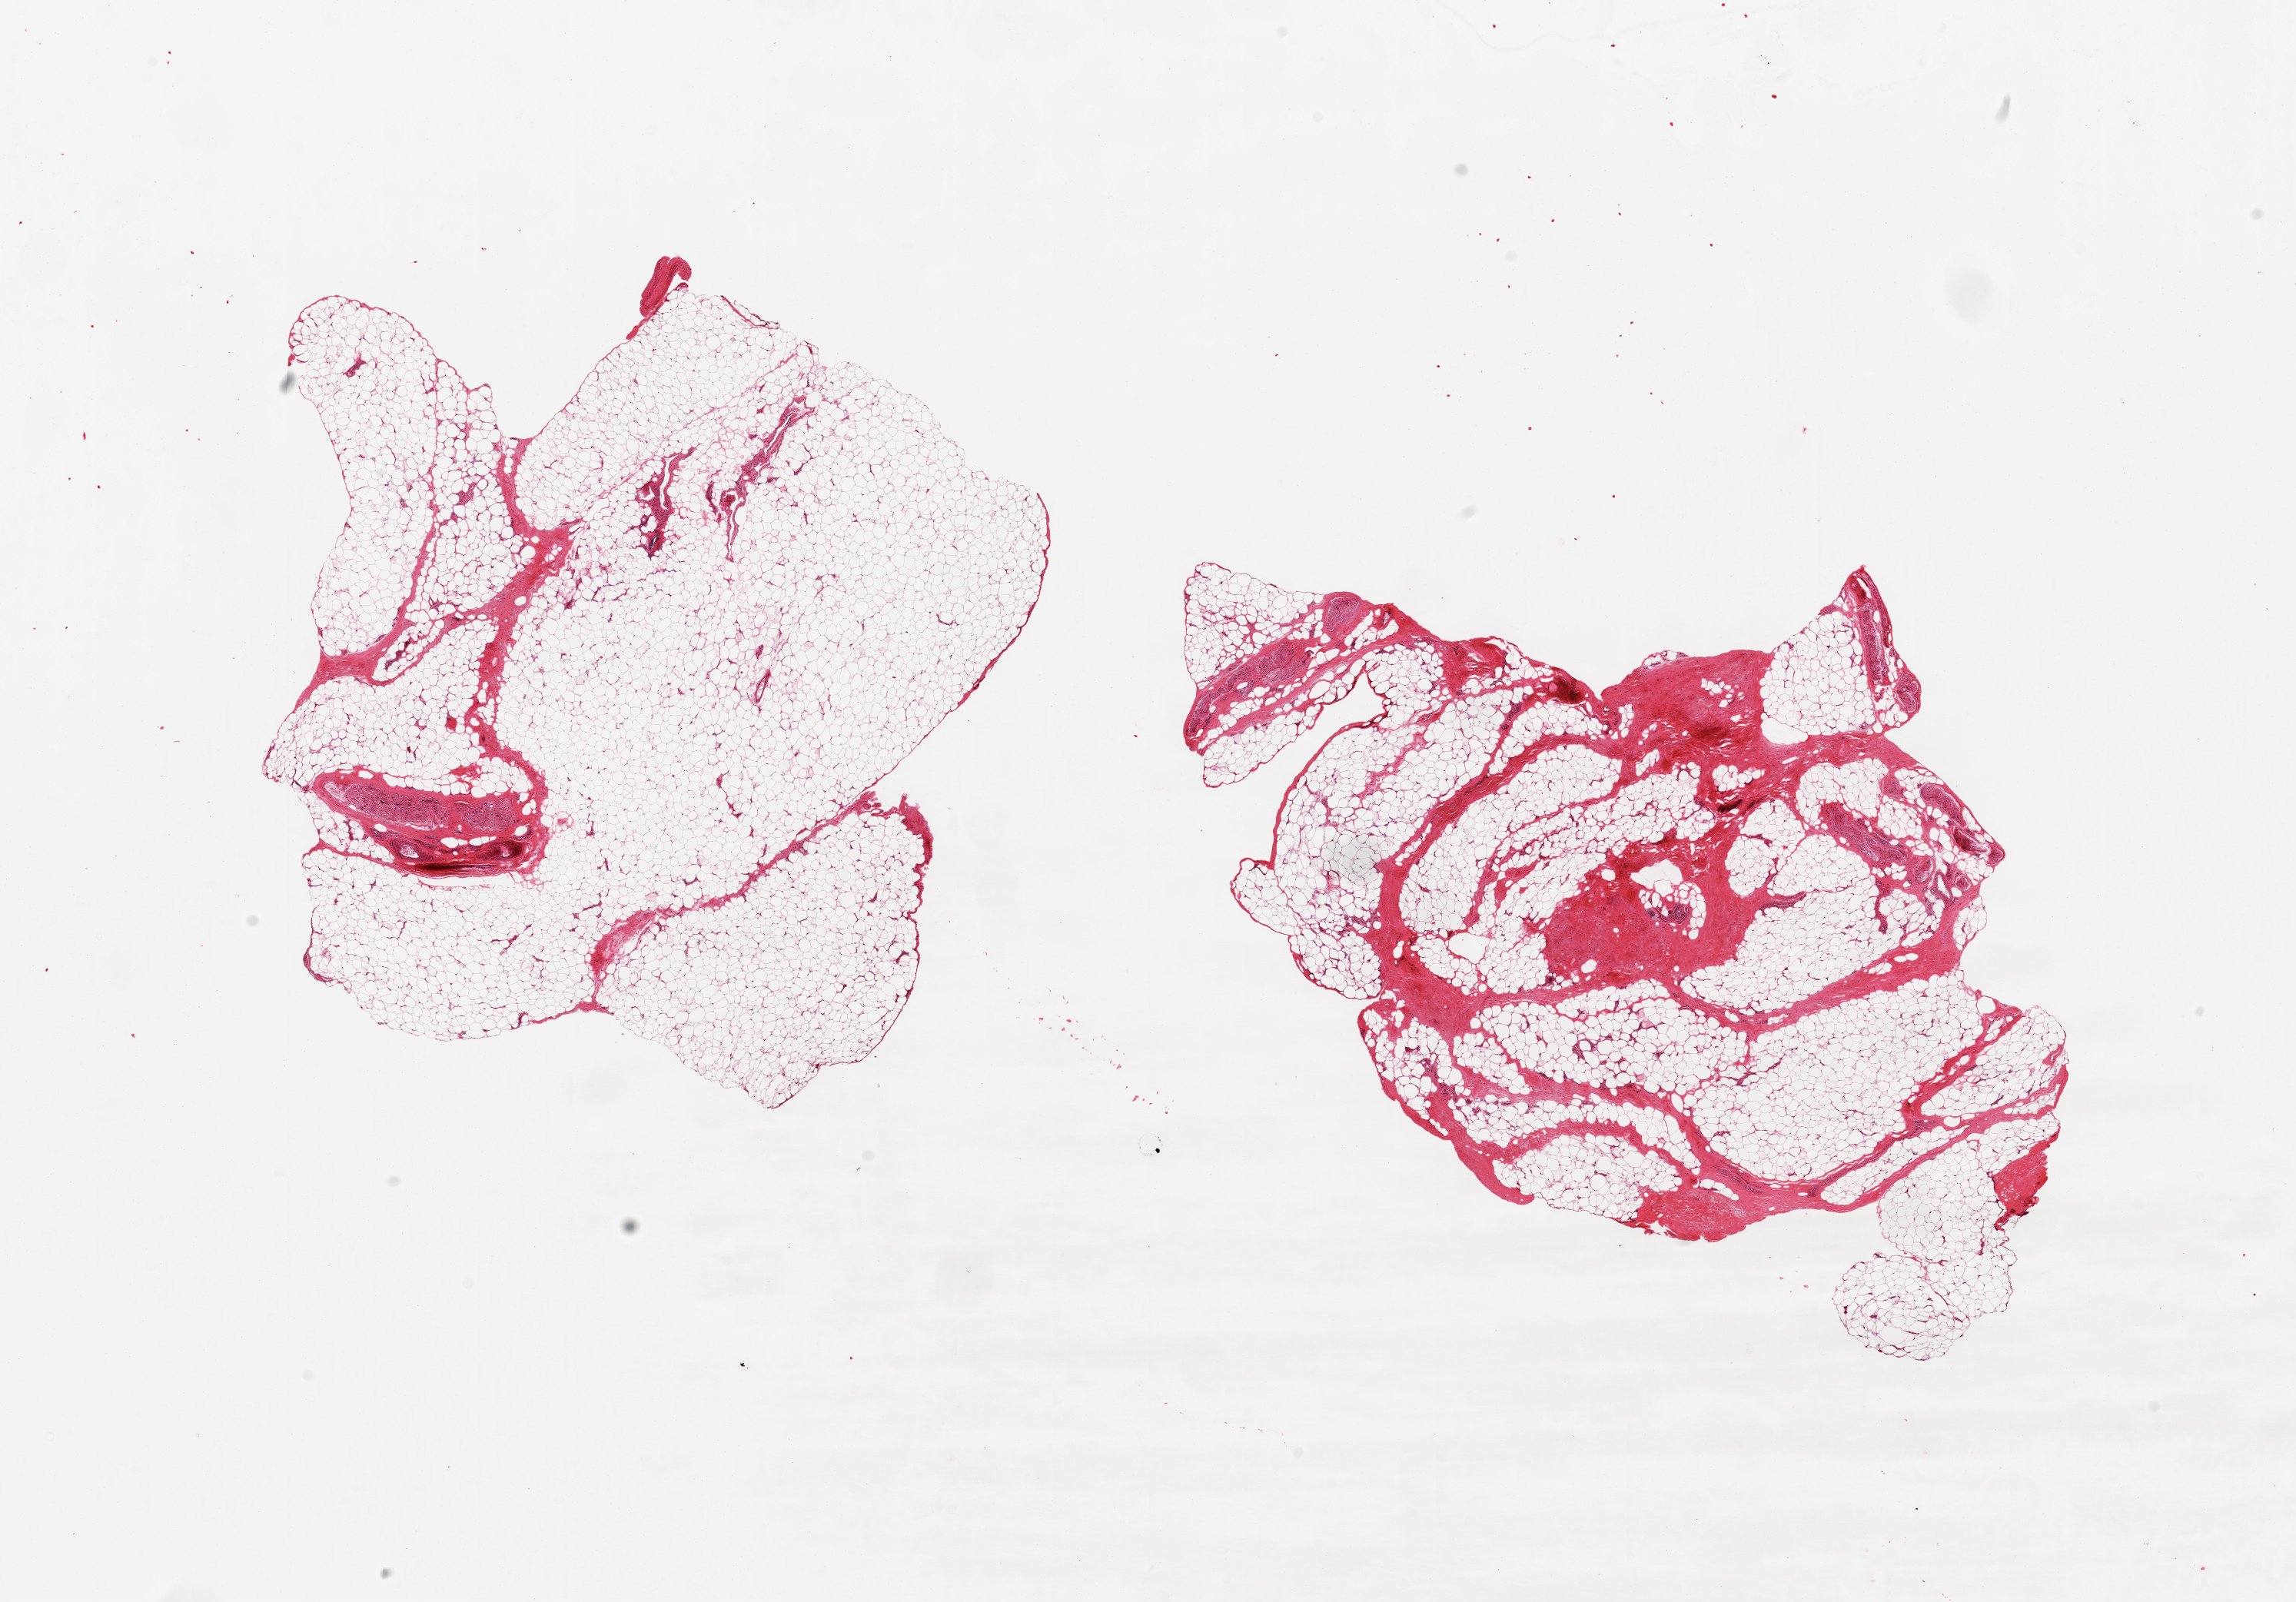
Hematoxylin and eosin (H&E) whole-slide image — low-resolution overview of the scanned area, about 23.6 x 16.5 mm (acquisition: 20x scan), PAXgene-fixed paraffin-embedded (PFPE) section, section of adipose tissue (target tissue), tissue donor sample. Donor: male.
Pathologist's review note for this sample: 2 pieces; ~10-20% fibrovascular tissue and nerve.